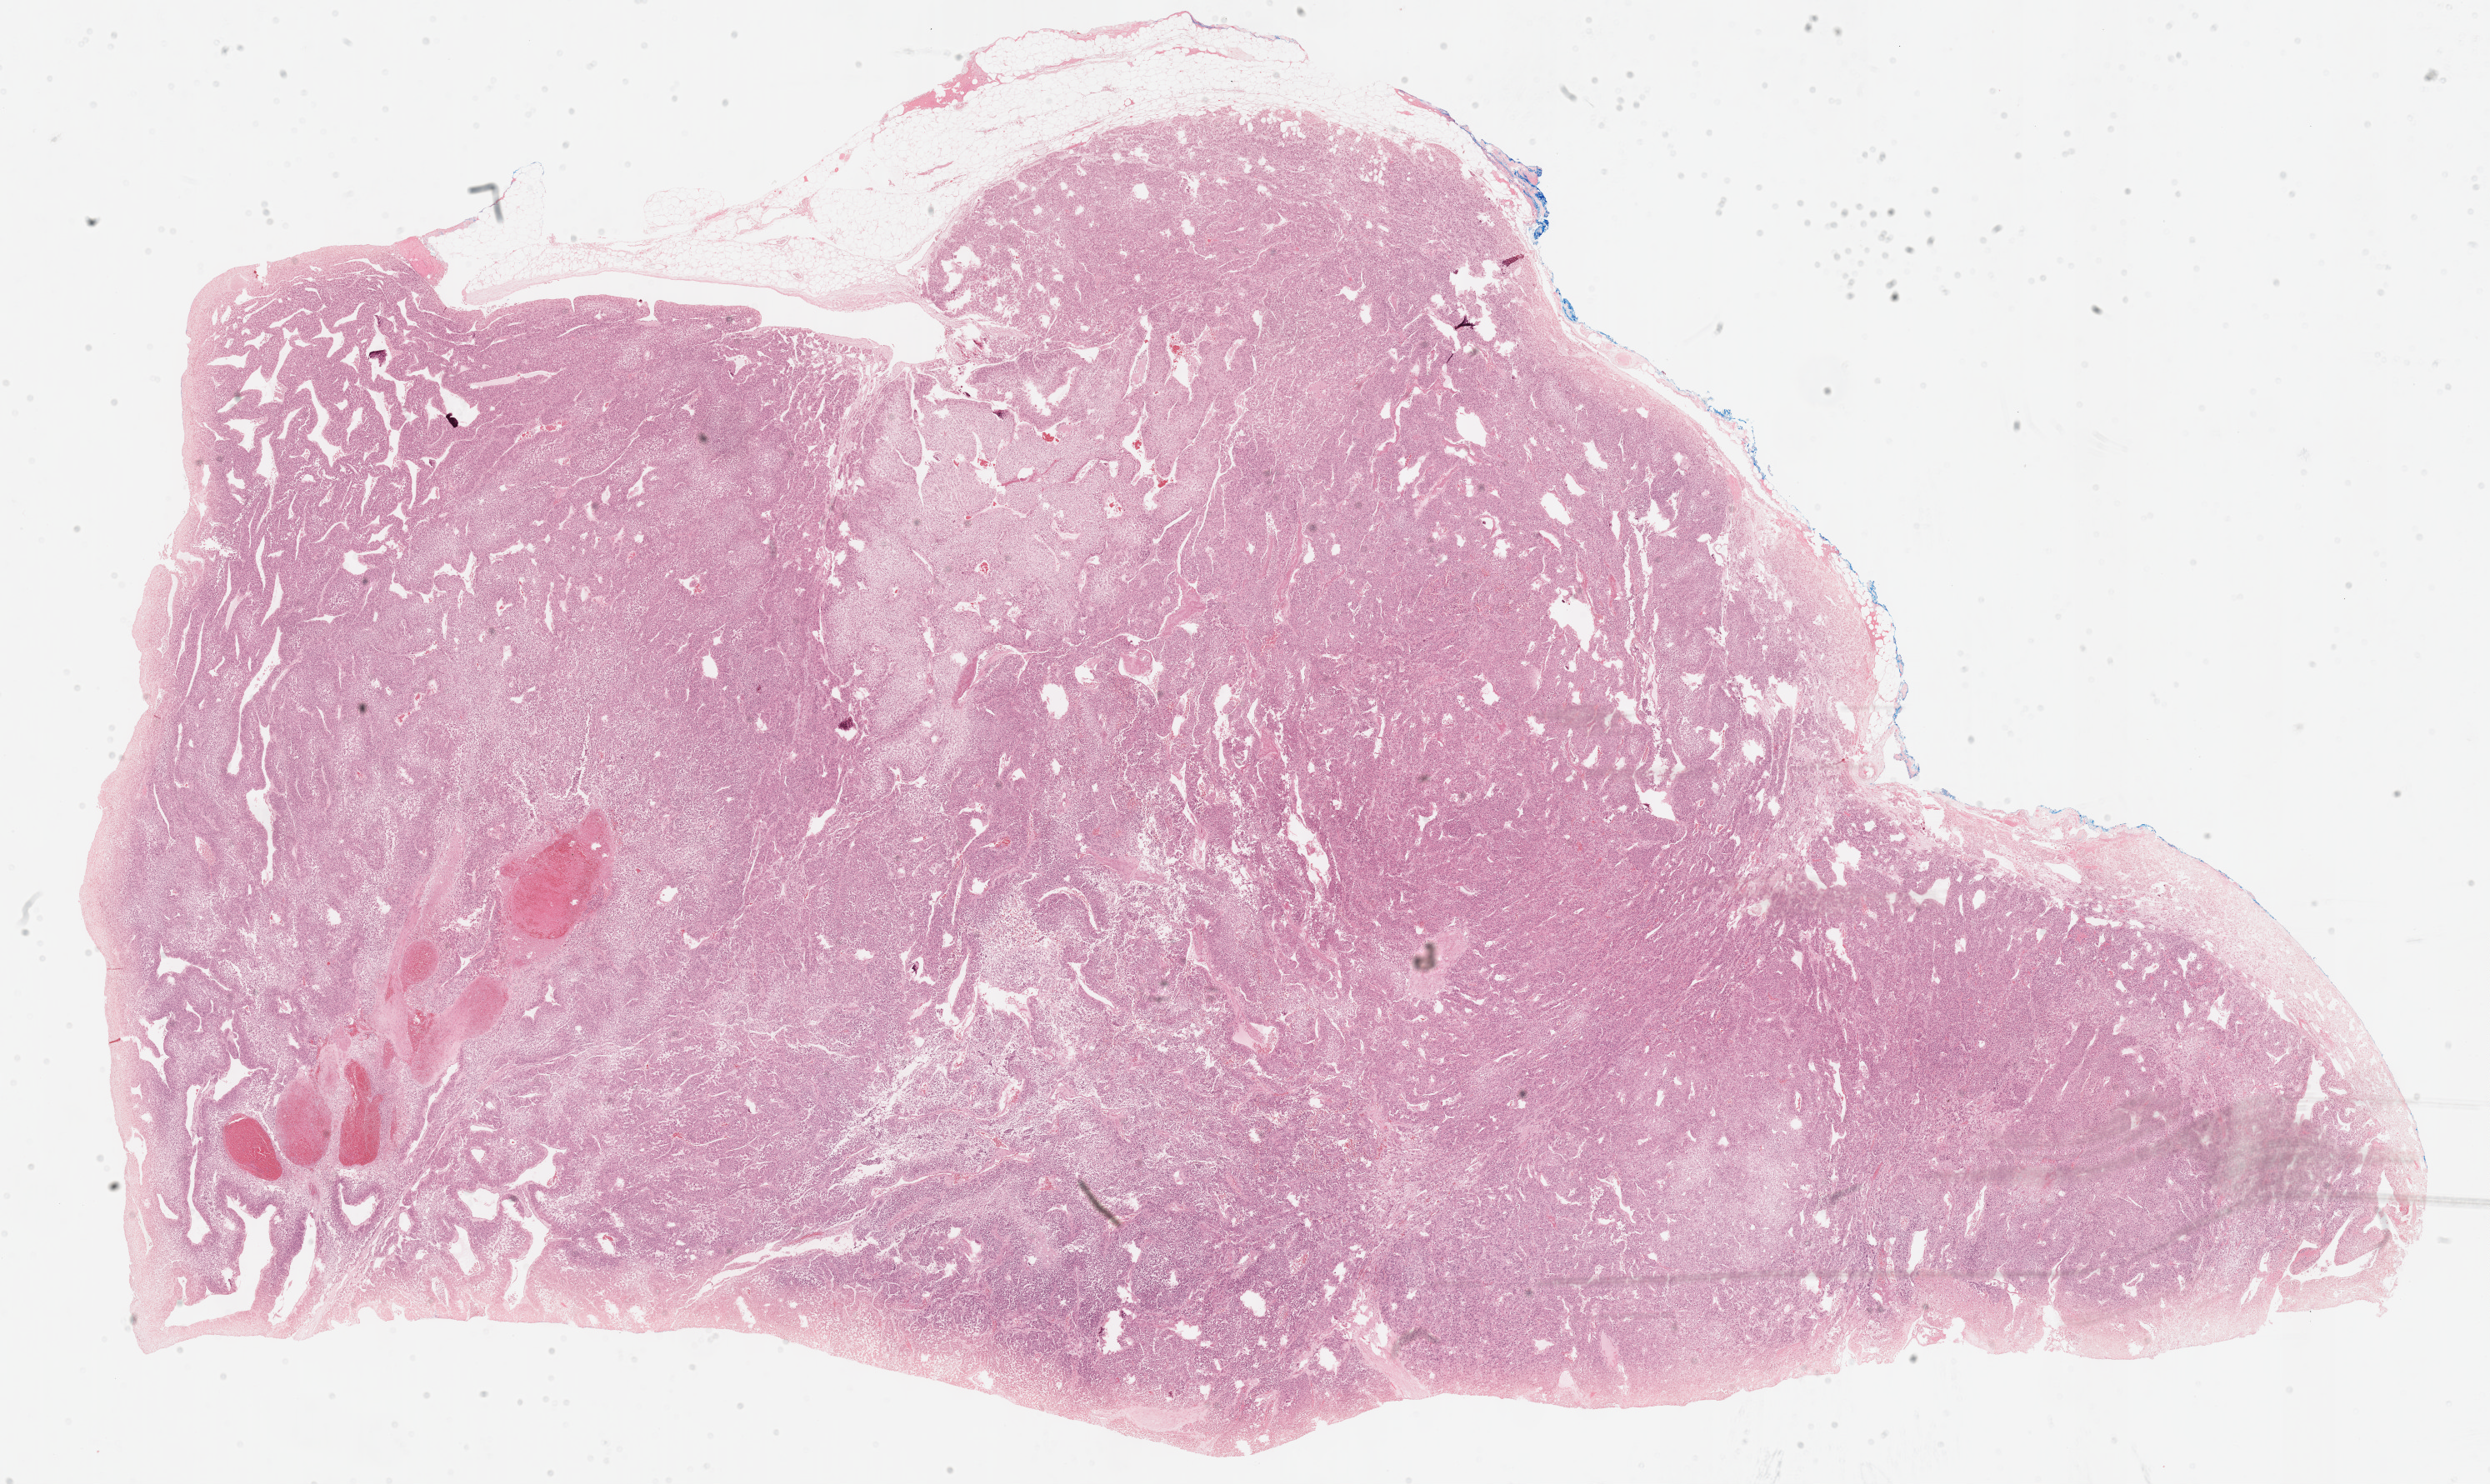
Hematoxylin and eosin (H&E) stained whole-slide image — low-resolution overview of the scanned area, about 24.1 x 14.4 mm (from a 40x scan). FFPE section. Primary tumour sample from the adrenal cortex. Patient: female, age at initial diagnosis 61 years.
Histologic diagnosis: Adrenal cortical carcinoma.